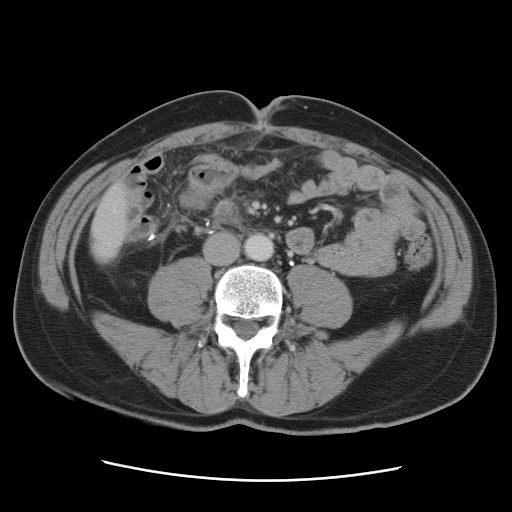
Contrast-enhanced abdominal CT, one axial slice; position 7 of 89 along the scan axis; 120 kVp; intravenous contrast given; soft-tissue window (W 400 / L 40 HU); 5 mm slice thickness; 512 × 512 image matrix, field of view 366 × 366 mm. Male patient, age 59 years. From the clinical record (not read from this slice): diagnosis: colorectal cancer liver metastases, imaged before liver resection.
Structures marked on this image (manually delineated by an expert):
- liver: bounding box <92,187,128,263> (left, top, right, bottom; pixels)
- planned liver remnant (the part of the liver to remain after resection): <91,186,128,259>